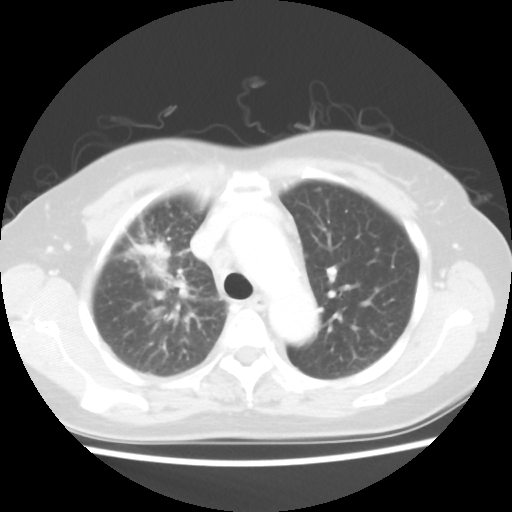
Chest CT, one axial slice; position 33 of 48 along the scan axis; lung window (W 1500 / L -600 HU); 512 × 512 image matrix. Female patient, age 55 years. Case-level facts recorded for this patient, not image findings: clinical TNM (as recorded): T1b N3 M1a.
Outlined on this slice (rectangle marked by the reading radiologist):
- lung tumour (recorded histology: adenocarcinoma): box from (x=132, y=239) to (x=170, y=260) px